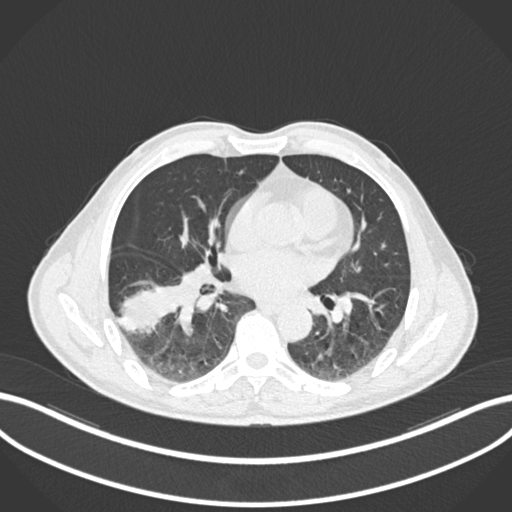
Chest CT, one axial slice; position 91 of 208 along the scan axis; reconstruction kernel B30f; lung window (W 1500 / L -600 HU); 1 mm slice thickness; 512 × 512 image matrix, field of view 400 × 400 mm. Patient: male, 58 years. From the clinical record (not read from this slice): clinical TNM (as recorded): T3 N0 M0.
Outlined on this slice (bounding box drawn by a radiologist):
- lung tumour (recorded histology: squamous cell carcinoma): bounding box (x1, y1, x2, y2) in pixels: (122, 276, 180, 341)